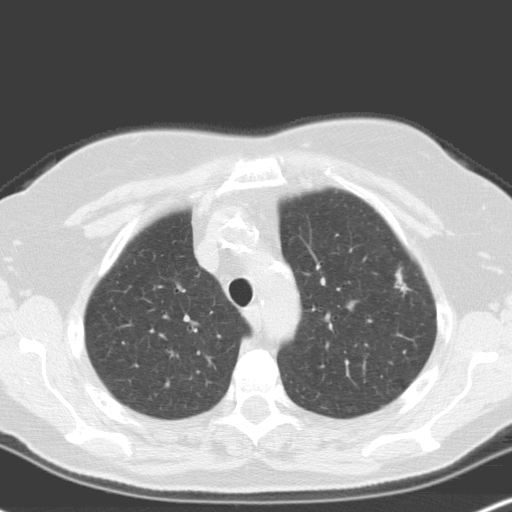
Low-dose screening chest CT, one axial slice; slice 132 of 160 in the series (ordered by position); 120 kVp; lung window (W 1500 / L -600 HU); 3.2 mm slice thickness; 512 × 512 image matrix, field of view 316 × 316 mm.
Annotated regions visible in this slice (outlined manually by an expert reader):
- lesion 2 (nodule): bounding box <396,272,408,291> (left, top, right, bottom; pixels)